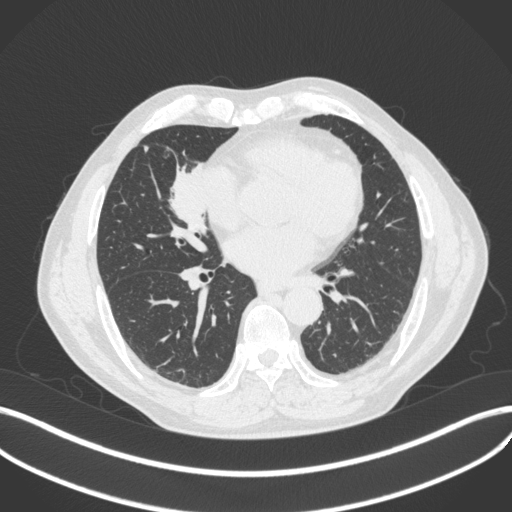
Chest CT, one axial slice; position 178 of 429 along the scan axis; lung window (W 1500 / L -600 HU); 512 × 512 image matrix, field of view 400 × 400 mm. Male patient, age 61 years. From the clinical record (not read from this slice): clinical TNM (as recorded): T2b N1 M0.
Outlined on this slice (rectangle marked by the reading radiologist):
- lung tumour (recorded histology: squamous cell carcinoma): box from (x=165, y=155) to (x=213, y=238) px